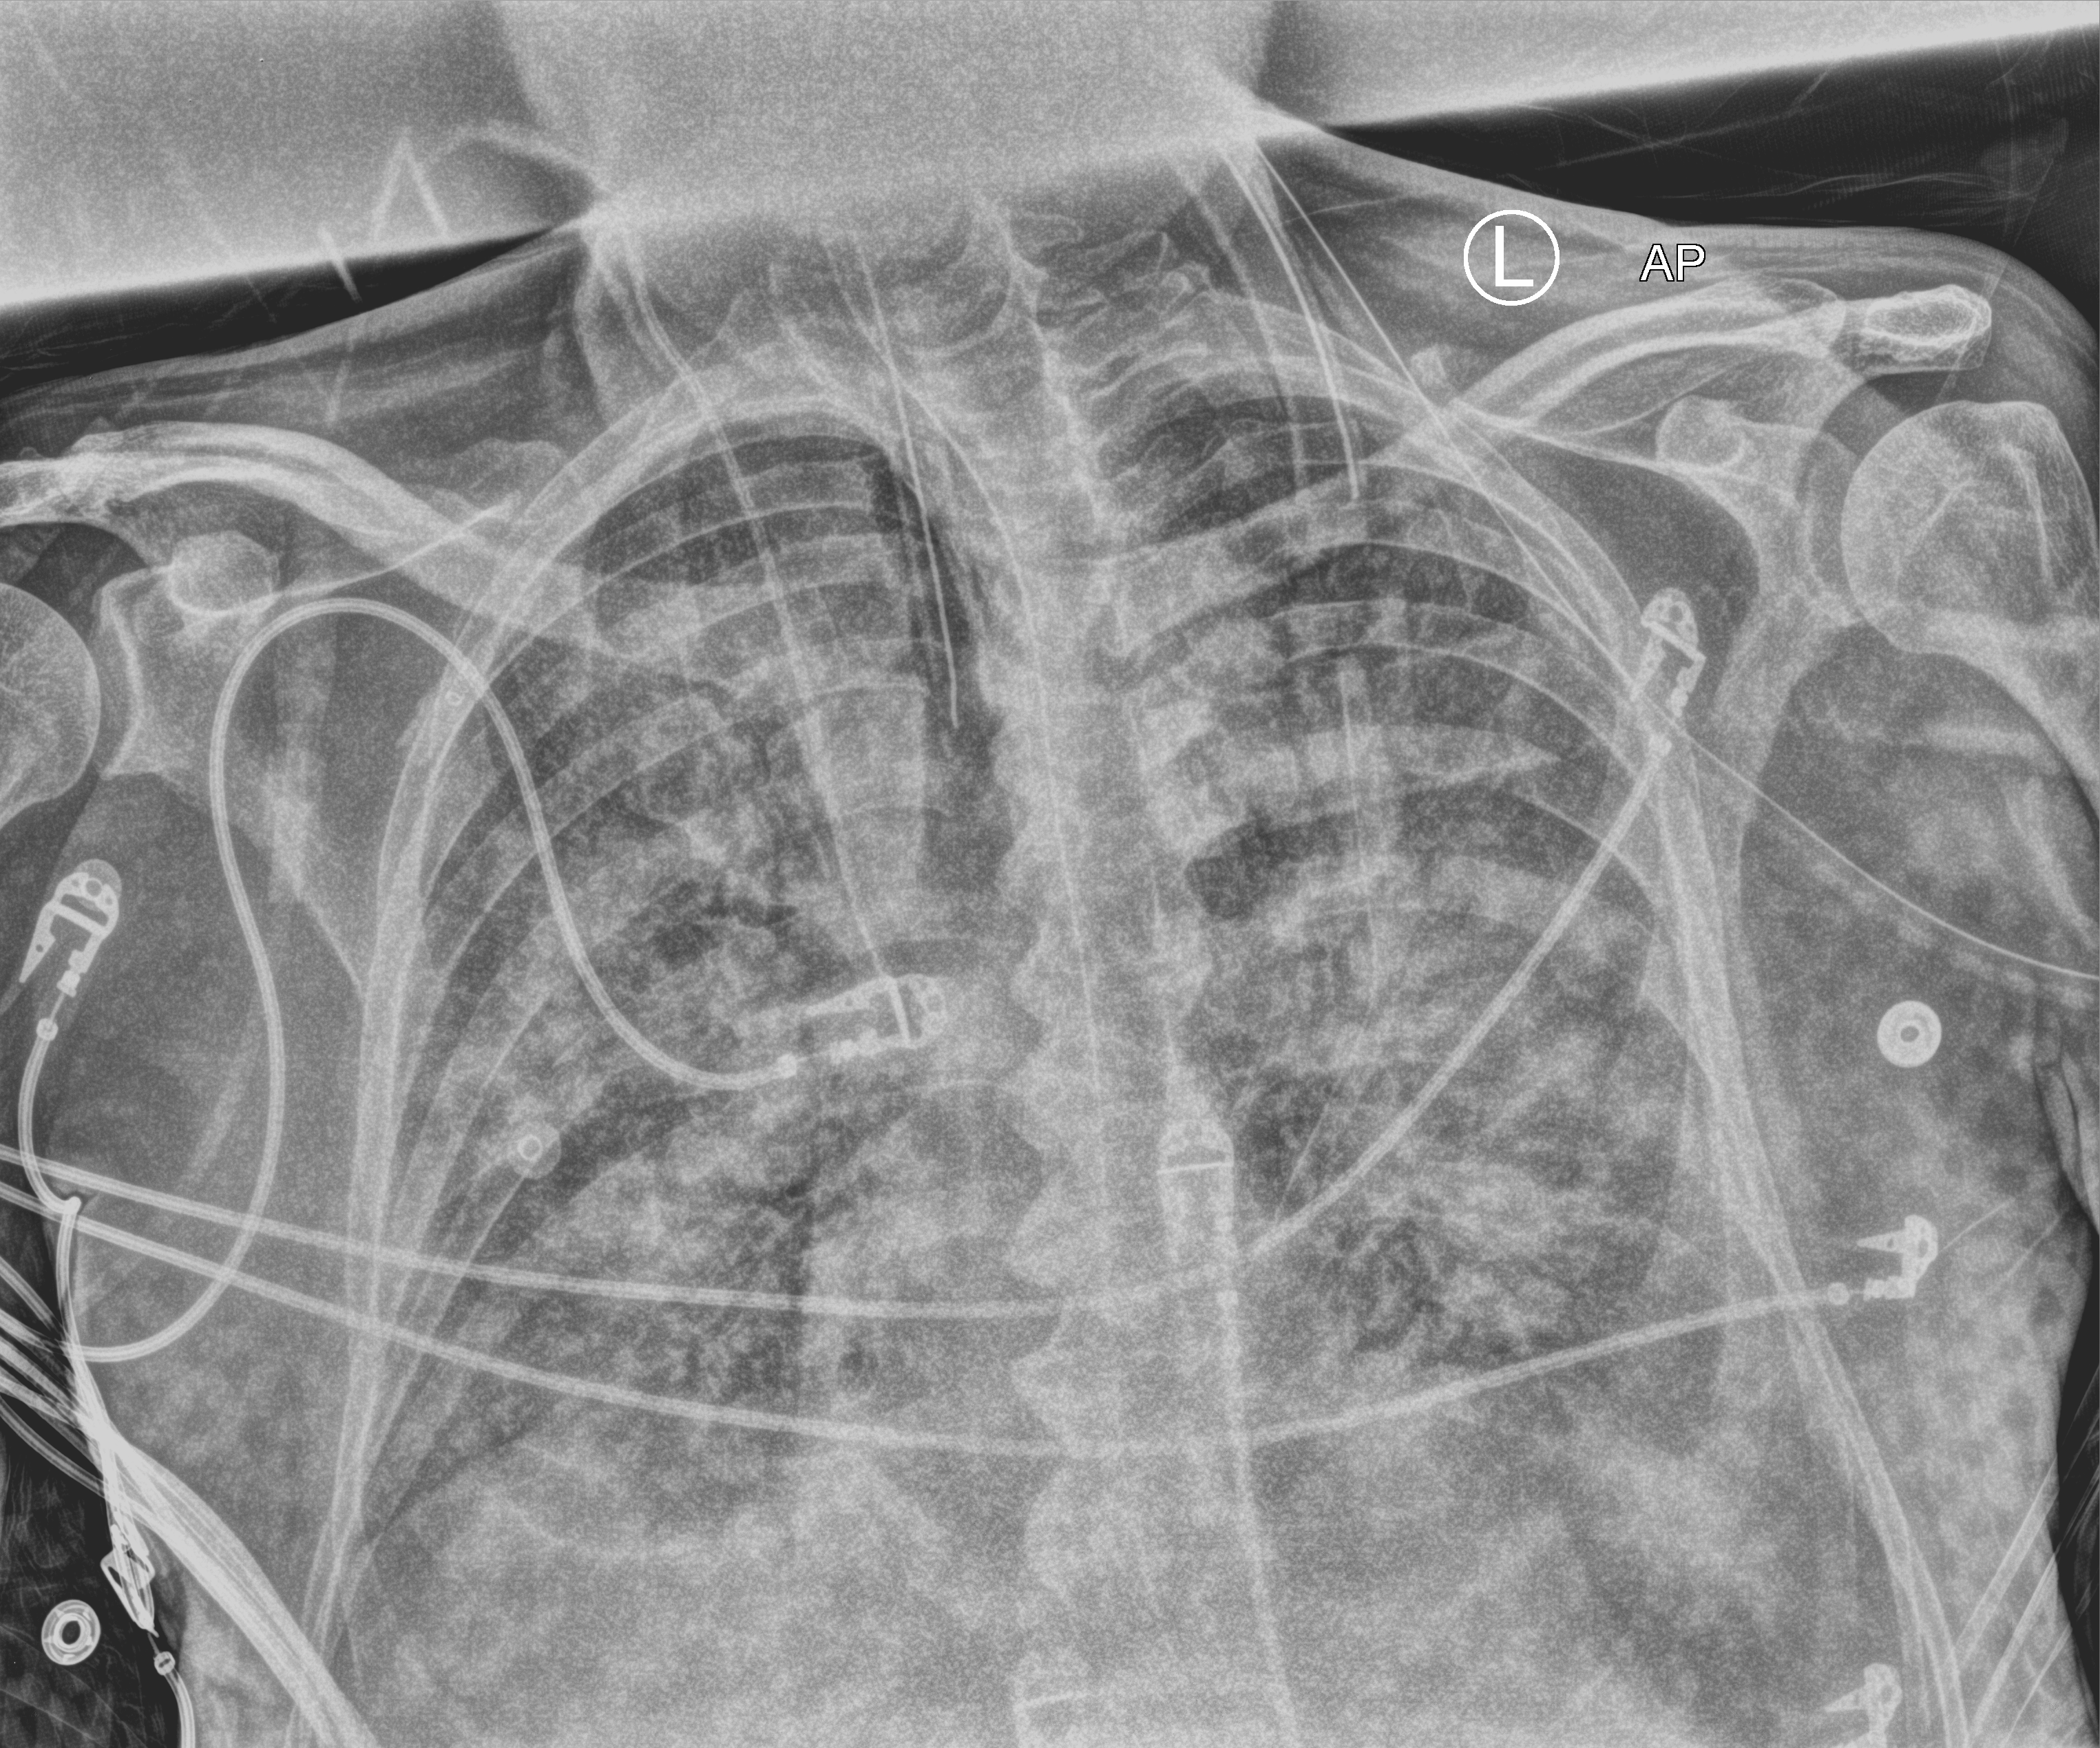
Portable chest radiograph. Patient hospitalised with COVID-19; male, aged 60–74 years.
From the hospital-stay record, not from the radiograph (when in the stay this image was taken is not recorded):
- COPD (admission record): no
- length of hospital stay: 15 days